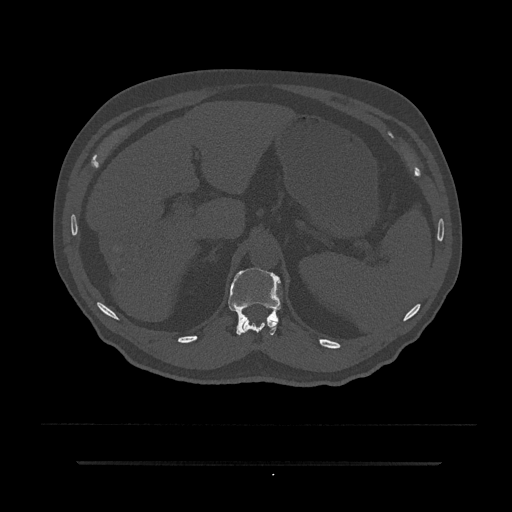
CT including the spine, one axial slice; position 236 of 797 along the scan axis; bone window (W 1800 / L 400 HU); 0.5 mm slice thickness; 512 × 512 image matrix, field of view 464 × 464 mm. Patient: male, 59 years. Case-level facts recorded for this patient, not image findings: primary cancer: bile ducts; vertebrae with lytic lesions (as recorded): T10.
Outlined on this slice (semi-automatic segmentation, software-assisted and operator-edited):
- T11 vertebra: box from (x=243, y=319) to (x=279, y=333) px
- T12 vertebra: (x=228, y=267)–(x=281, y=336)